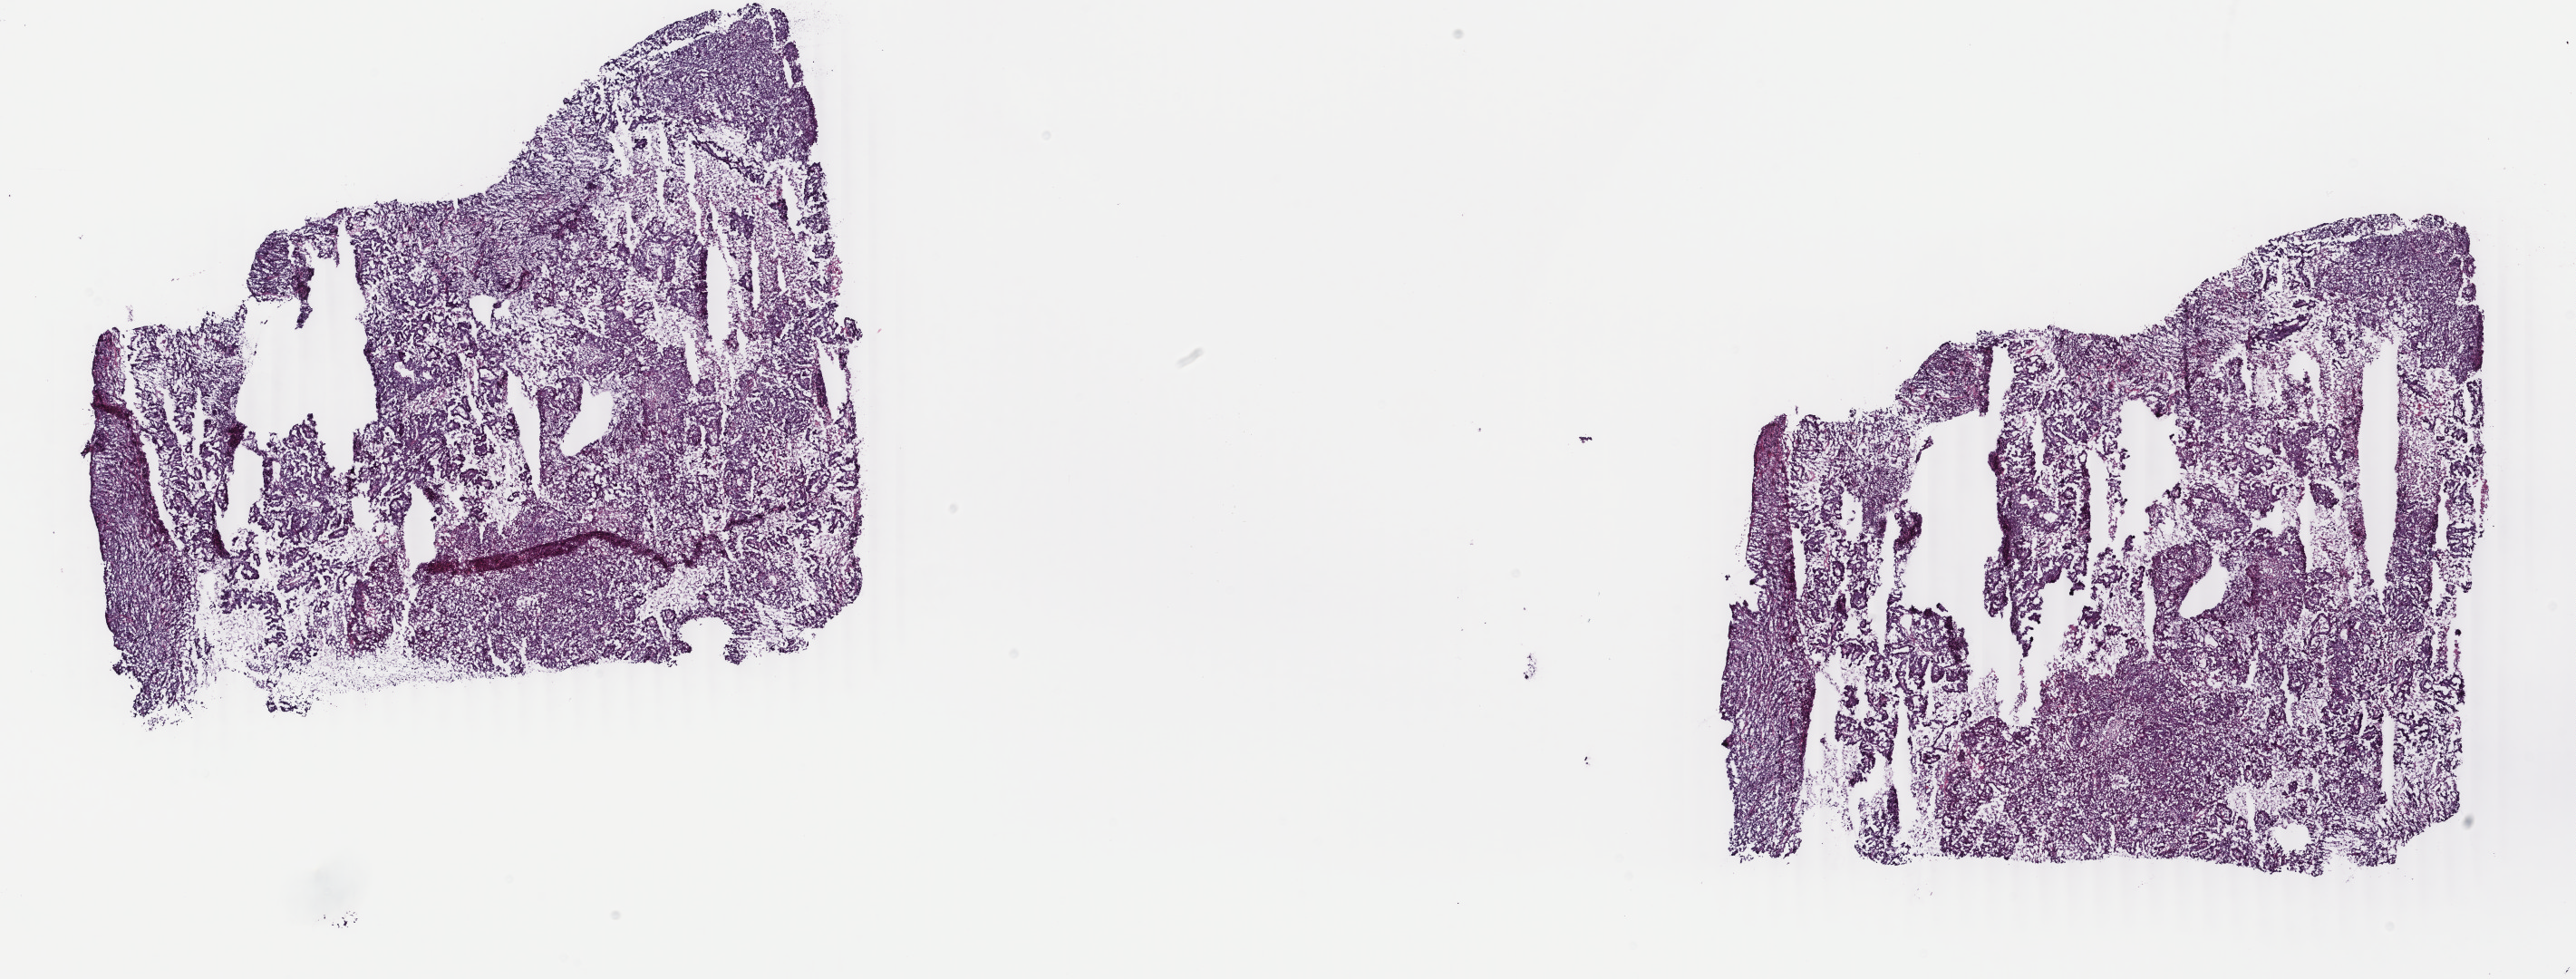
Digitized H&E-stained tissue section (whole slide) — a low-resolution overview of the entire scanned area, about 22.6 x 8.6 mm (from a 40x scan); frozen section from the top of the tissue portion; primary tumour sample from the uterus. Female, age 62 years at initial diagnosis. Histologic grade: high grade. Pathologist review of this section (percent, as recorded): tumour cells 80%, tumour nuclei 90%, normal cells 0%, stromal cells 15%, necrosis 5%. Infiltration values recorded for this section: lymphocyte infiltration 0%, monocyte infiltration 0%, neutrophil infiltration 0%.
Lymph nodes positive (case pathology): 0 of 22 examined. FIGO stage: IC. Pathologic diagnosis: Serous cystadenocarcinoma, NOS (endometrium).